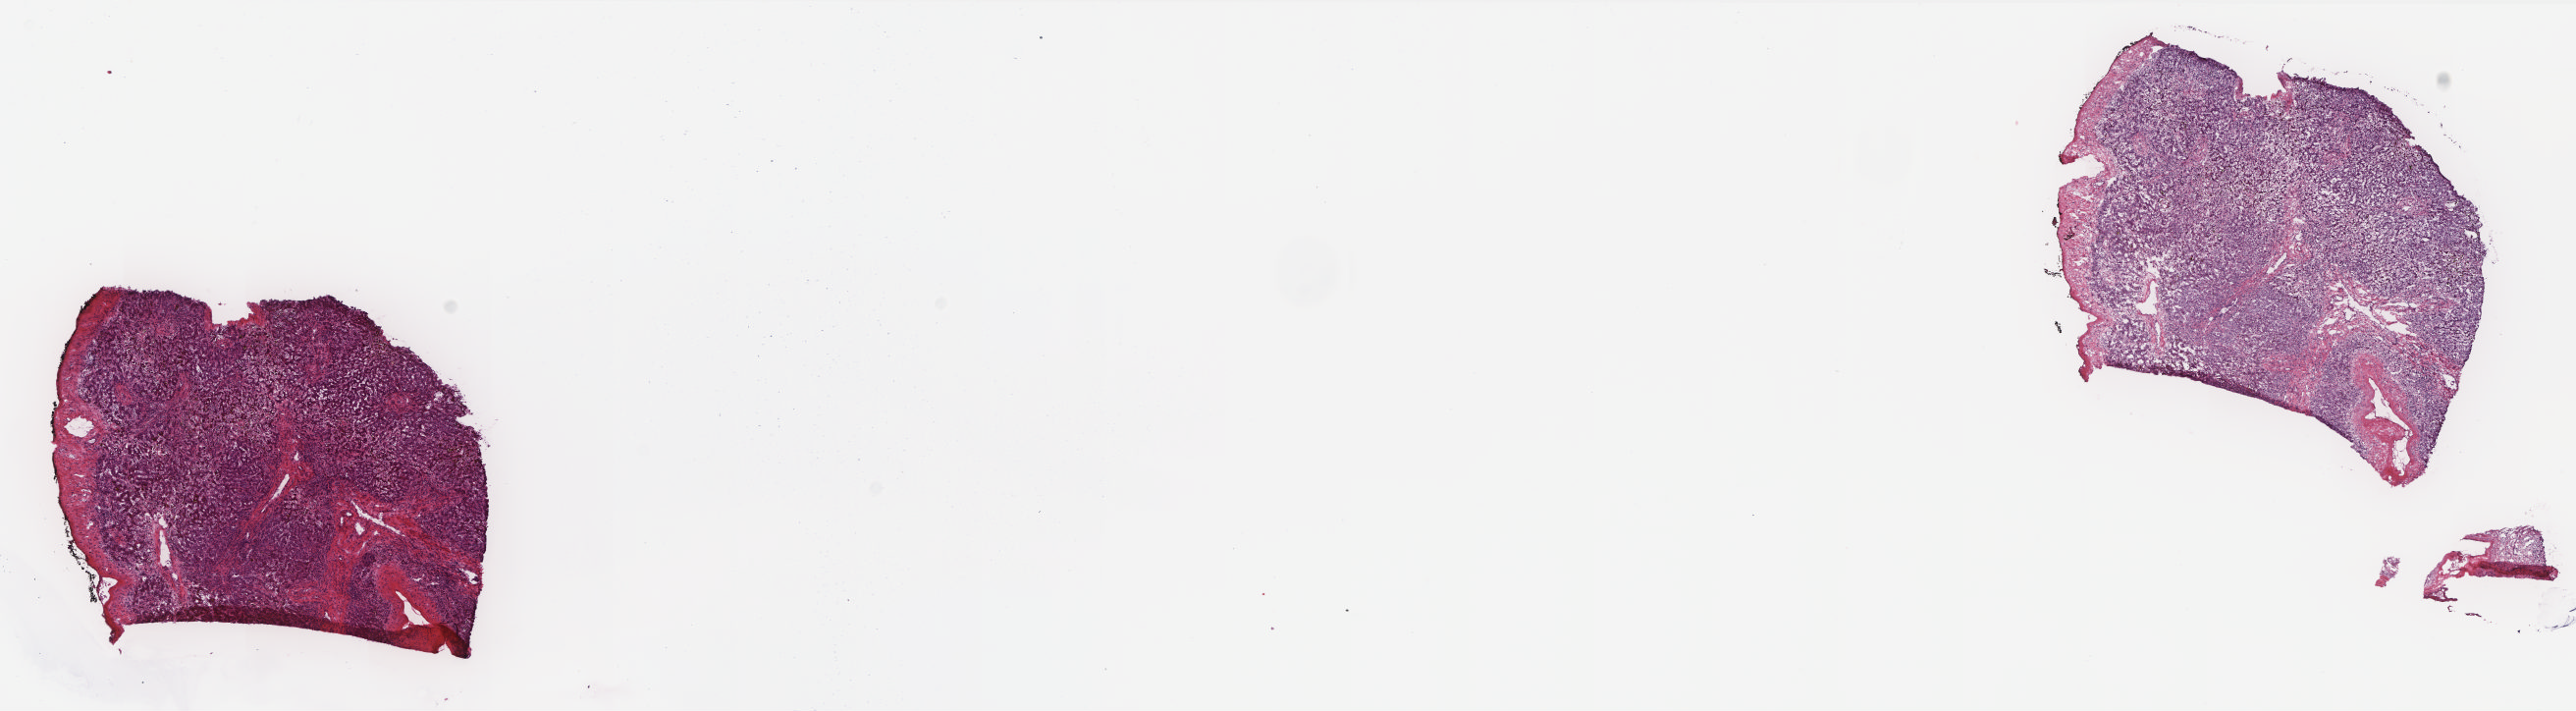
H&E-stained whole-slide image — whole scanned area (about 21.0 x 5.8 mm, from a 20x scan) shown as a low-resolution overview. Frozen section. Sample: solid tissue normal (non-tumour tissue), liver. Patient: male, age at initial diagnosis 75 years. Slide review estimates, as recorded: tumour cells 0%, tumour nuclei 0%, normal cells 85%, stromal cells 15%, necrosis 0%. Inflammatory infiltration, as recorded: lymphocyte infiltration 4%, monocyte infiltration 0%, neutrophil infiltration 0%.
This section: solid tissue normal sample (biorepository sample class). Patient diagnosis: Hepatocellular carcinoma, NOS.